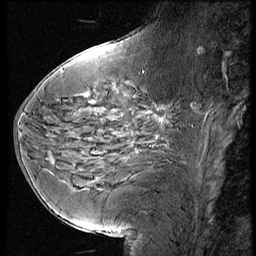
Breast MRI (dynamic contrast-enhanced), one sagittal slice. Slice 23 of 60 in the series (ordered by position). 3 images stored at this slice position (order not interpretable as contrast timing). 1.5 T. TE 4.2 ms, TR 9 ms. 256 × 256 image matrix. Female patient, age 56 years. Case-level facts recorded for this patient, not image findings: setting: breast cancer imaged before/during neoadjuvant chemotherapy.
Outlined on this slice (semi-automatic segmentation, software-assisted and operator-edited):
- analysis volume of interest (the breast-tissue region the enhancement analysis was run in; not a lesion): bounding box <137,61,218,137> (left, top, right, bottom; pixels)
- tumour enhancement mask (voxels above the 140 % enhancement threshold inside the analysis volume of interest): <192,104,194,106>